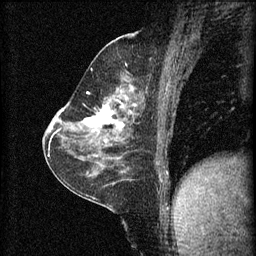
Breast MRI (dynamic contrast-enhanced), one sagittal slice; position 32 of 60 along the scan axis; 3 images stored at this slice position (order not interpretable as contrast timing); 1.5 T; TE 4.2 ms, TR 8.2 ms; 2 mm slice thickness; 256 × 256 image matrix, field of view 180 × 180 mm. Female patient, age 59 years.
Annotated regions visible in this slice (semi-automatic segmentation, software-assisted and operator-edited):
- analysis volume of interest (the breast-tissue region the enhancement analysis was run in; not a lesion): bounding box <78,92,137,135> (left, top, right, bottom; pixels)
- tumour enhancement mask (voxels above the 70 % enhancement threshold inside the analysis volume of interest): <84,100,135,127>